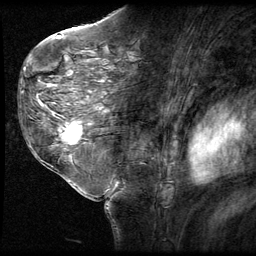
Breast MRI (dynamic contrast-enhanced), one sagittal slice. Slice 35 of 58 in the series (ordered by position). 3 images stored at this slice position (order not interpretable as contrast timing). 1.5 T. TE 4.2 ms, TR 9 ms. 2.5 mm slice thickness. 256 × 256 image matrix. Patient: female, 58 years. Case-level facts recorded for this patient, not image findings: setting: breast cancer imaged before/during neoadjuvant chemotherapy; receptor status: HR-positive, HER2-negative.
Annotated regions visible in this slice (semi-automatic segmentation, software-assisted and operator-edited):
- analysis volume of interest (the breast-tissue region the enhancement analysis was run in; not a lesion): bounding box <51,116,93,151> (left, top, right, bottom; pixels)
- tumour enhancement mask (voxels above the 140 % enhancement threshold inside the analysis volume of interest): <59,122,83,145>